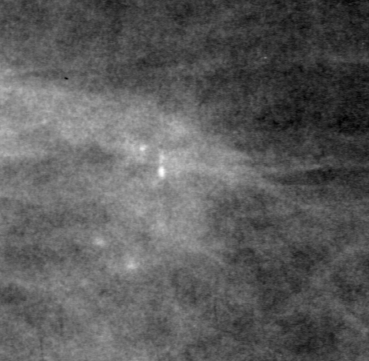
Crop from a digitized film mammogram around one marked abnormality, right breast, CC view.
- Calcifications, morphology pleomorphic, distribution clustered; BI-RADS assessment category 4; subtlety rating 3 on a 1 (subtle) to 5 (obvious) scale; pathology result (as recorded, not read from the image): malignant.